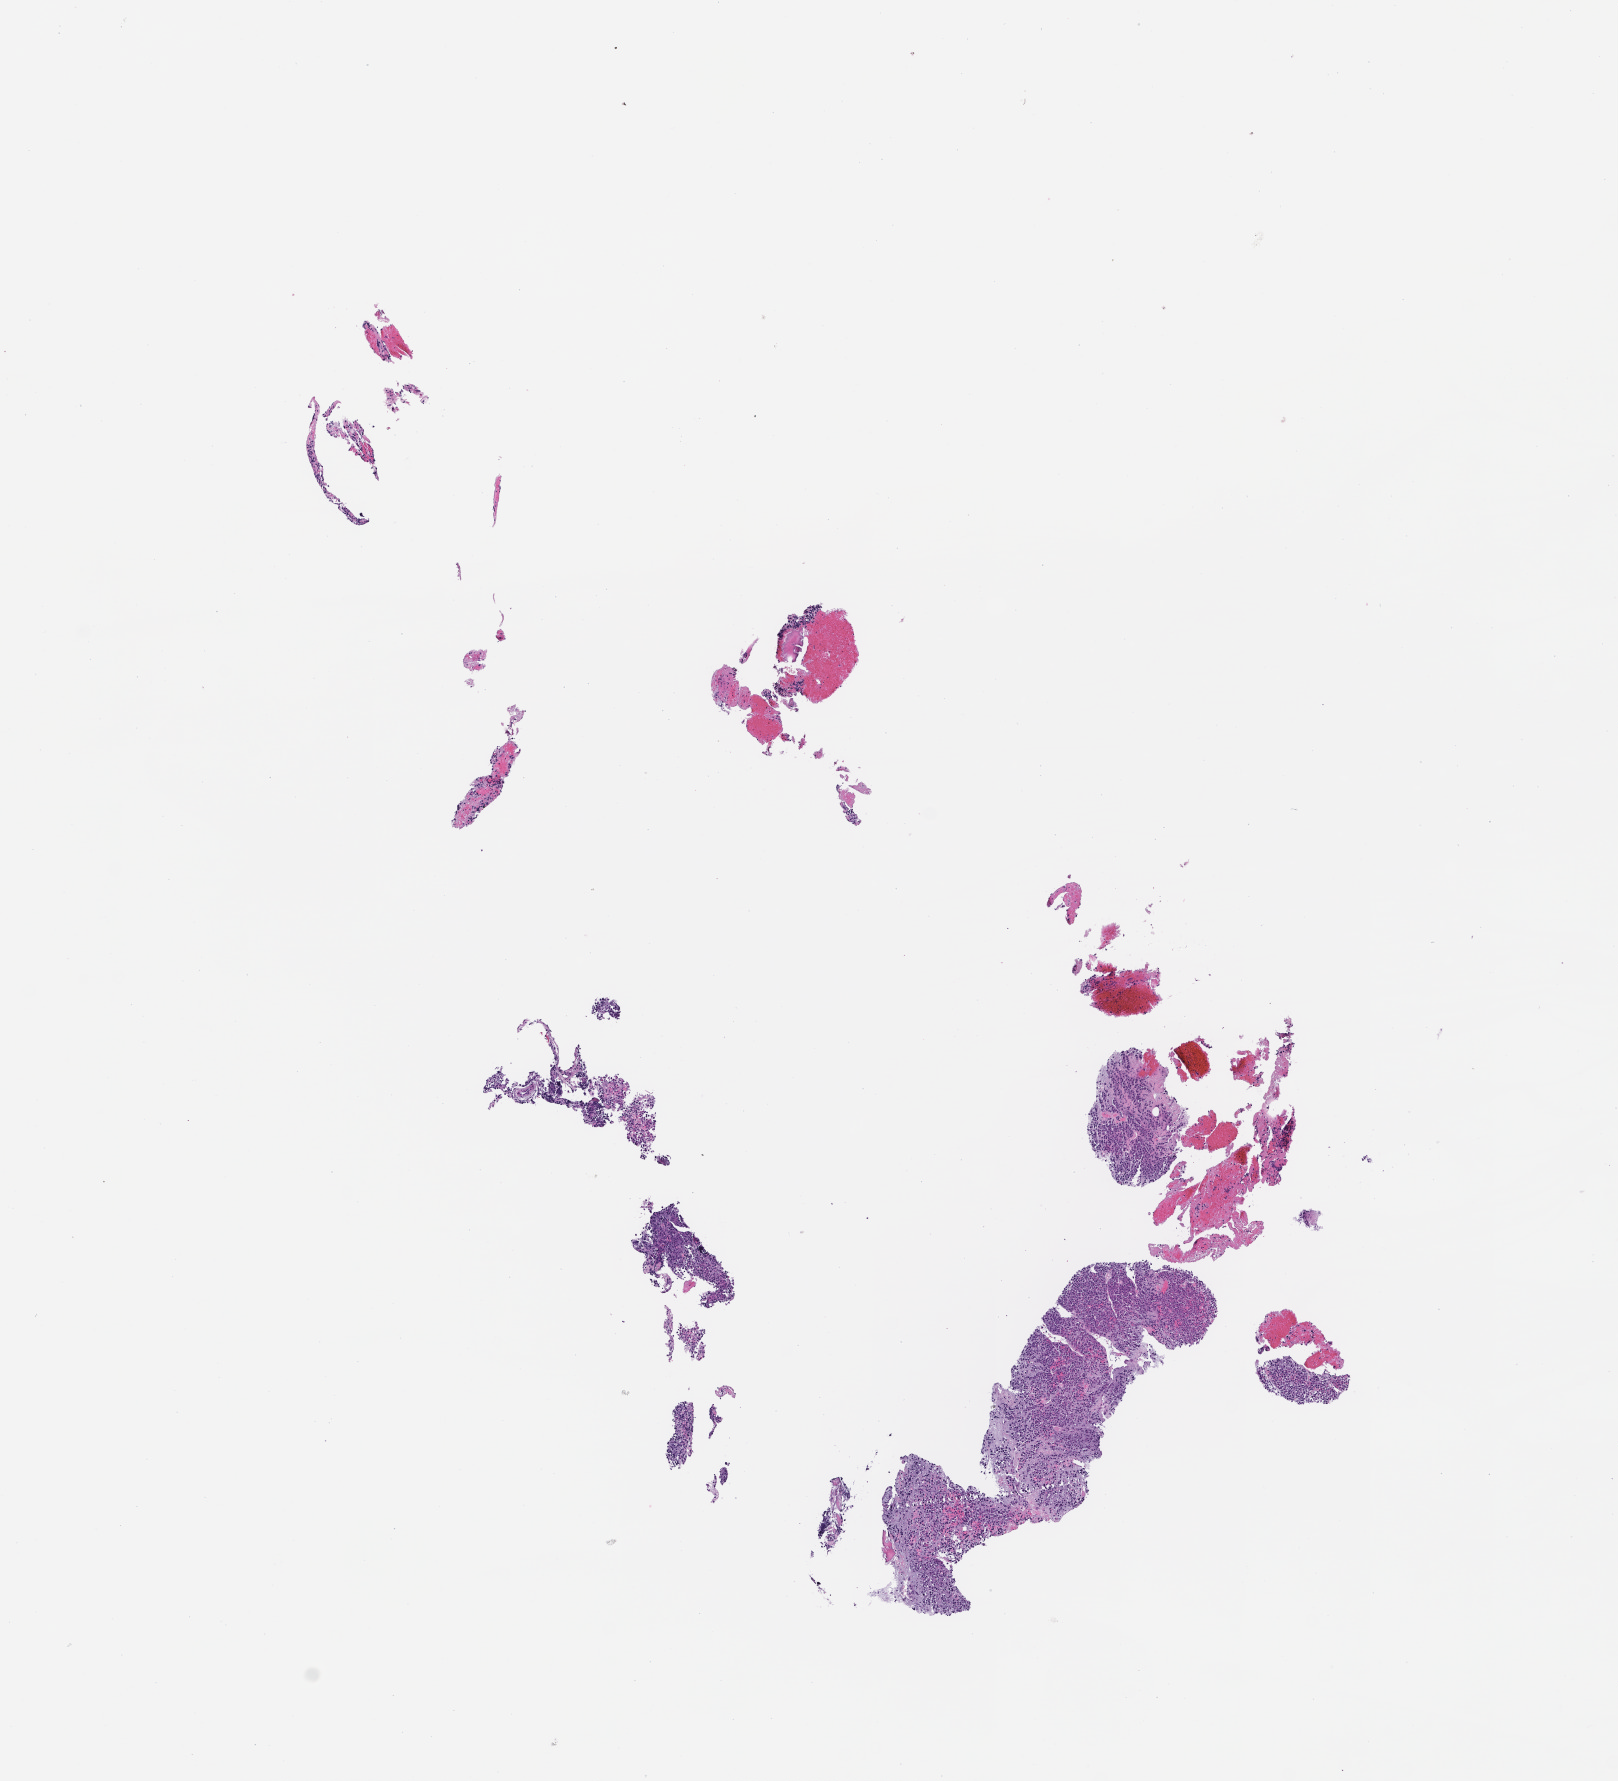
Whole-slide image, H&E stain, shown as a low-resolution overview of the whole scanned area (about 6.5 x 7.2 mm); formalin-fixed paraffin-embedded section; archival tissue. Patient: female.
This section: metastatic tumor tissue. Patient diagnosis (primary): Plasma Cell Myeloma.